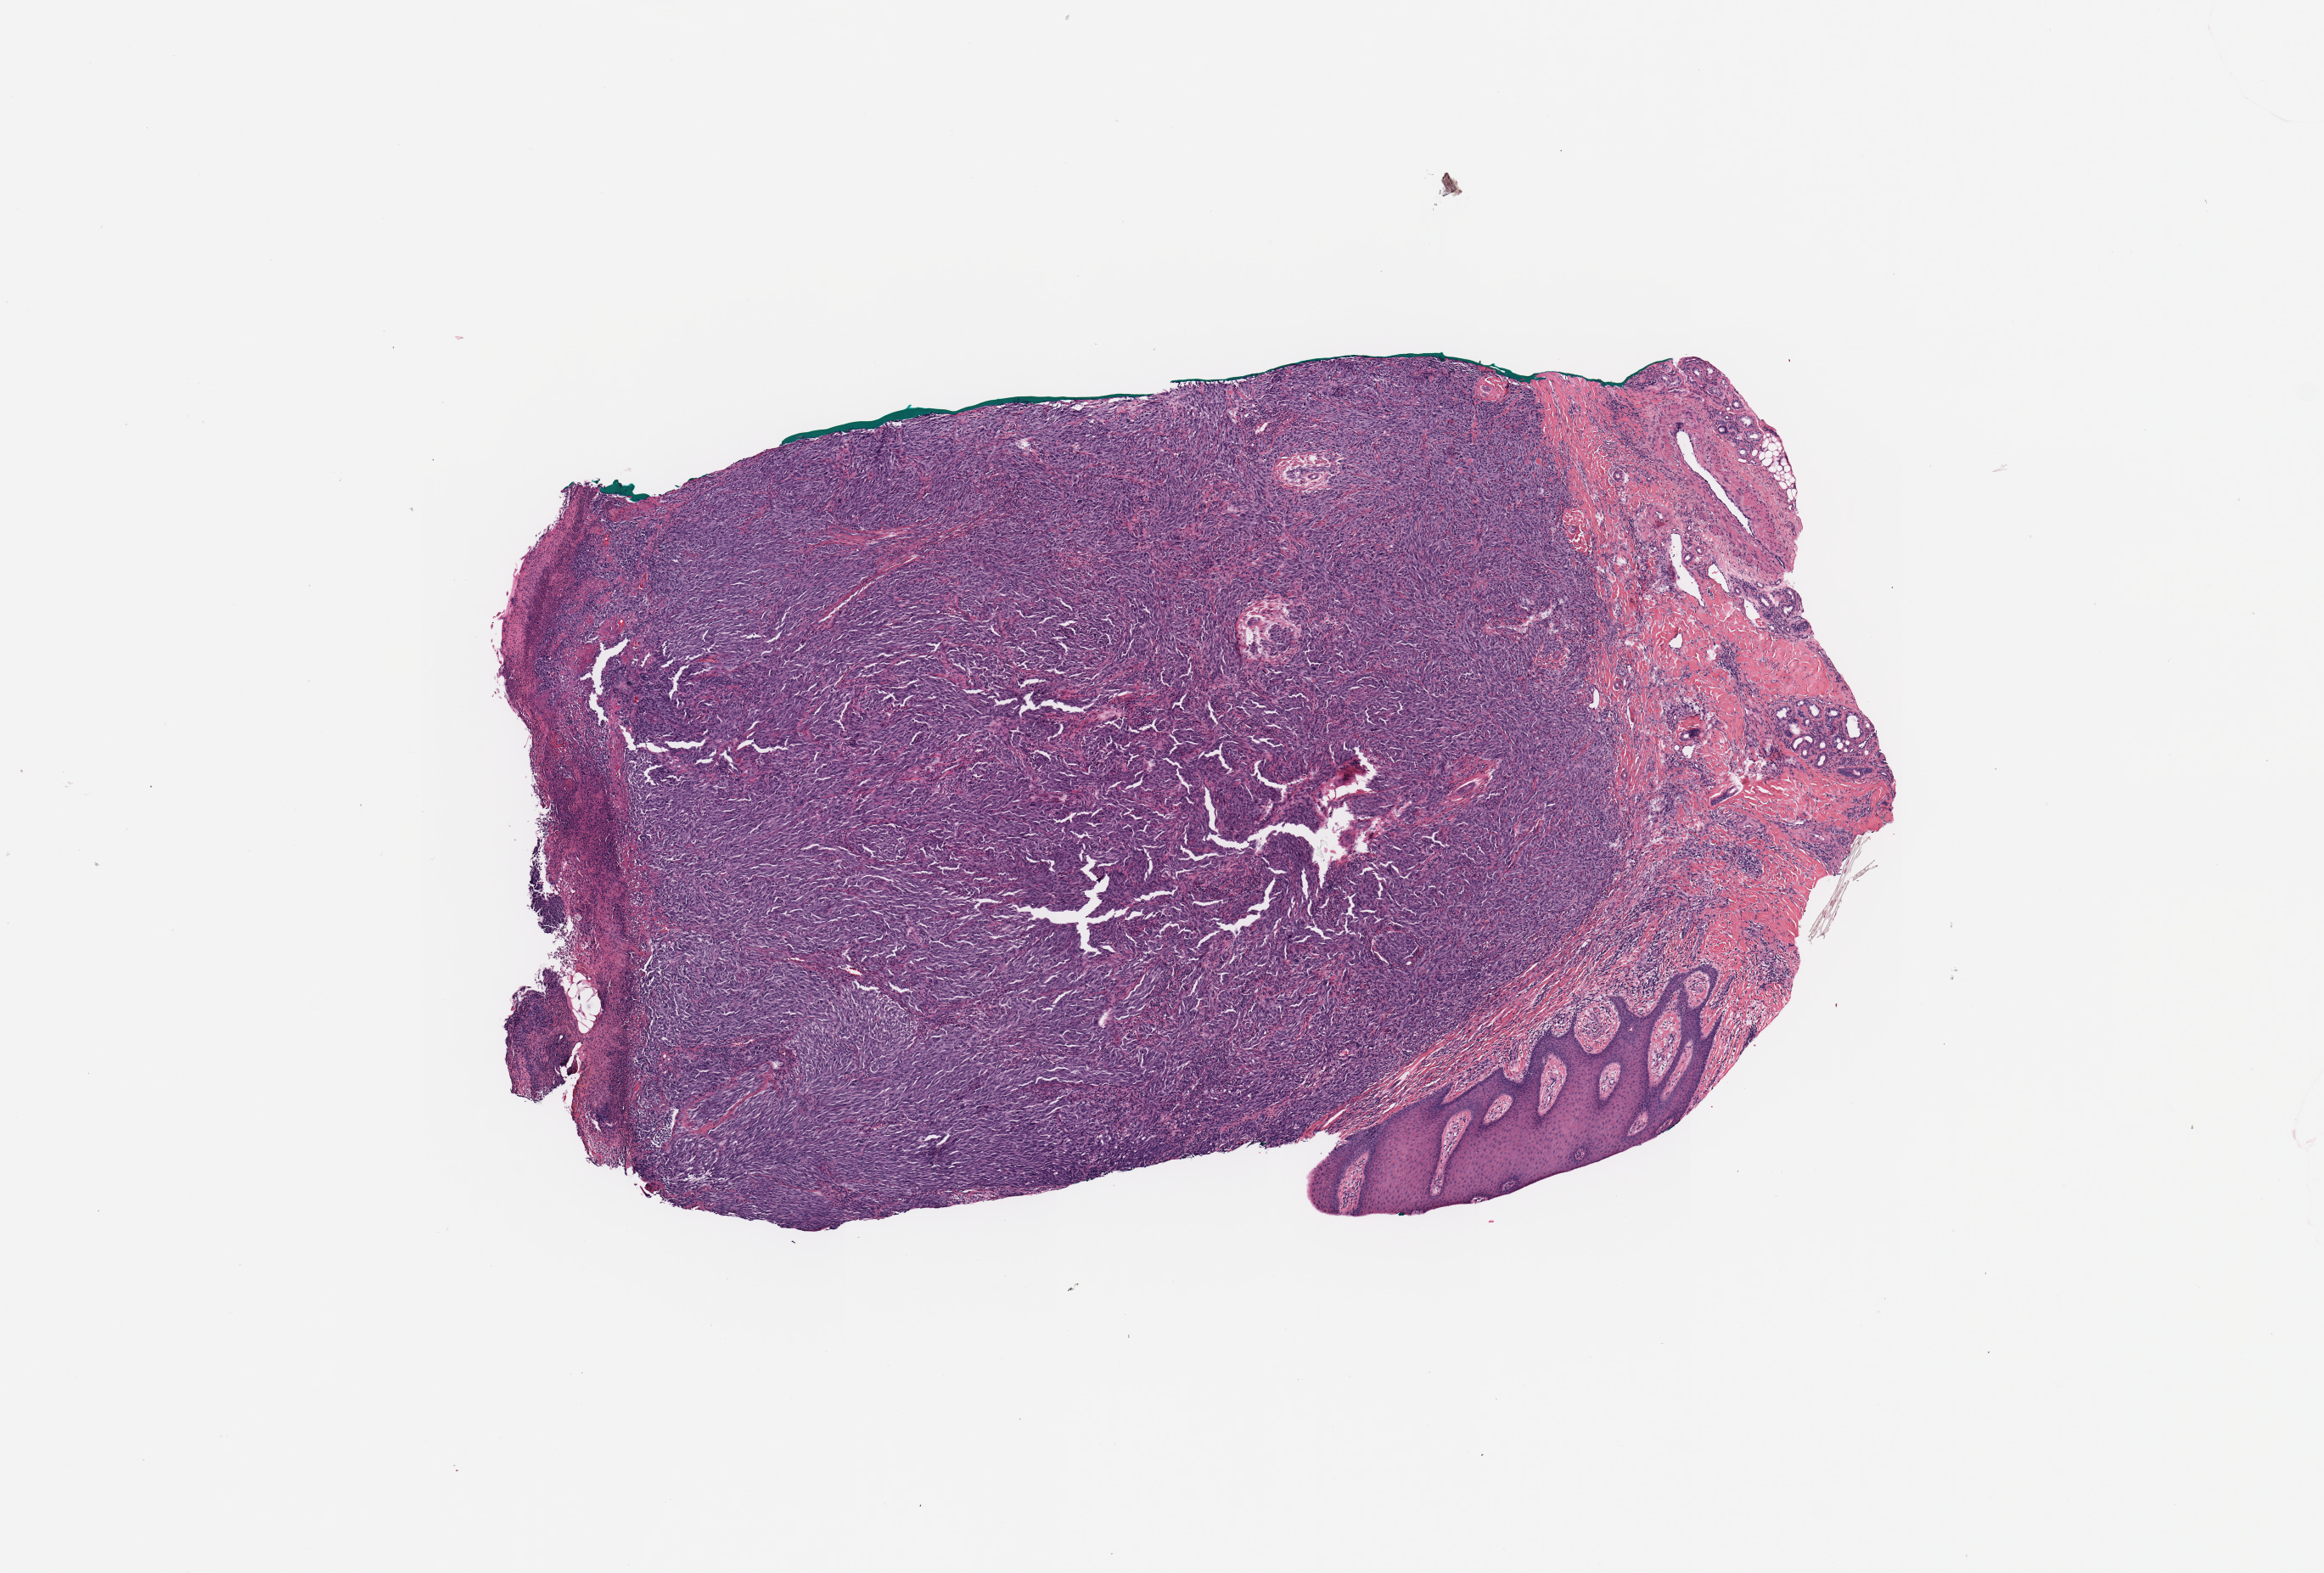
Digitized H&E-stained tissue section (whole slide), whole scanned area (about 10.8 x 7.3 mm, slide scanned at 20x) shown as a low-resolution overview, tumour tissue sample, sampled site: skin. 71-year-old male patient. Pathologist review of this section (percent, as recorded): tumour nuclei 80%, necrosis 5%.
• AJCC pathologic stage: IIC
• histologic diagnosis: Malignant melanoma, NOS
• primary tumour site (as recorded): palms and soles